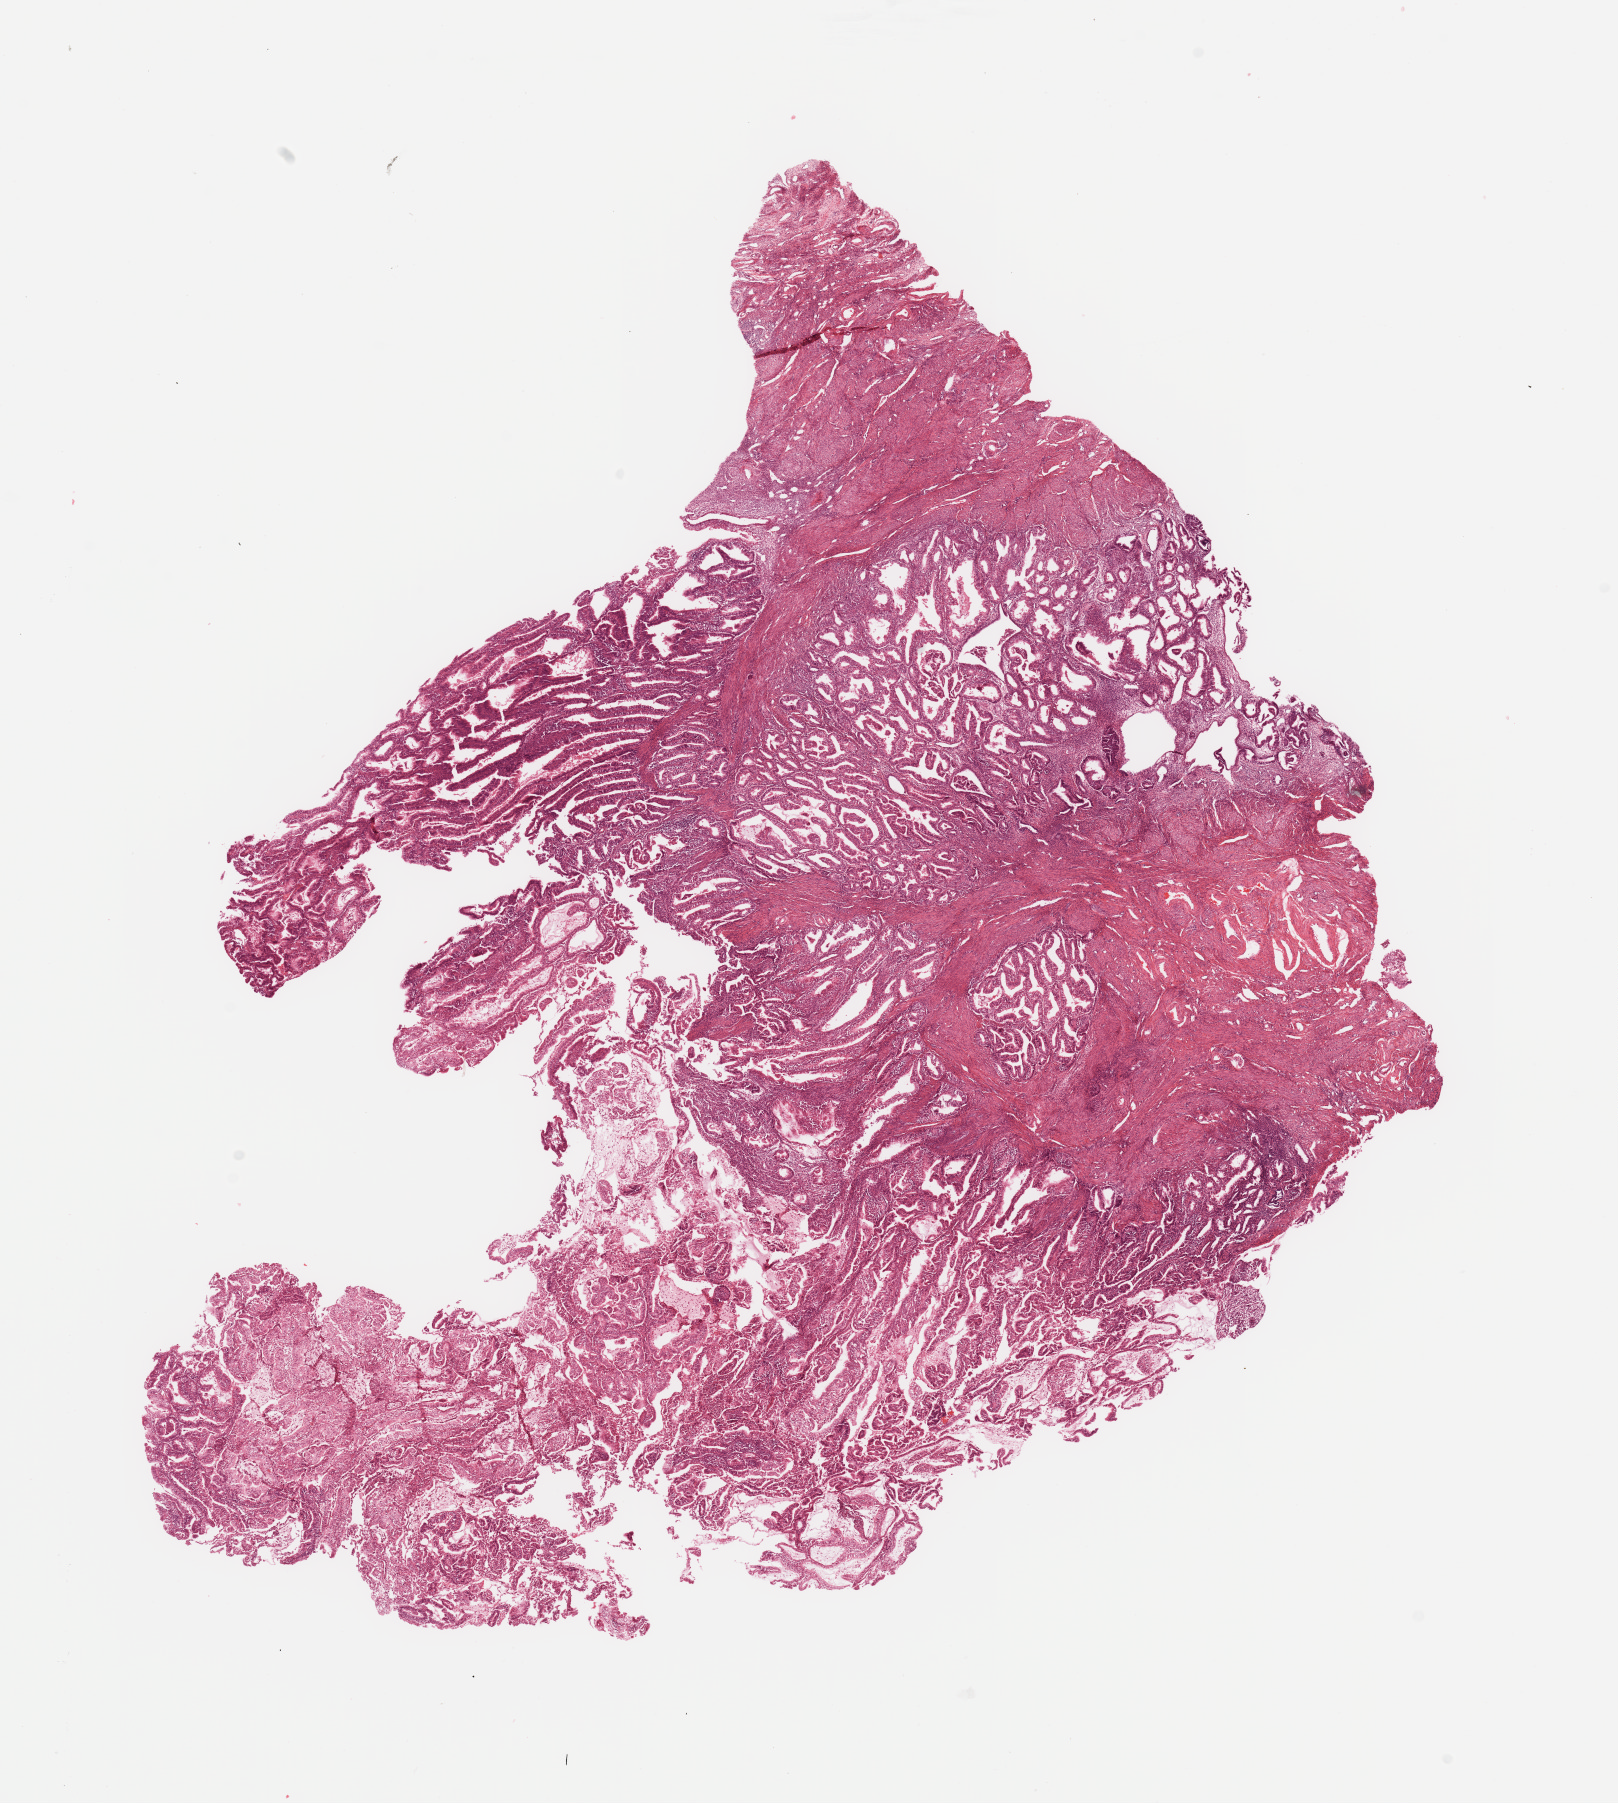
H&E whole-slide image — whole scanned area (about 12.8 x 14.3 mm) shown as a low-resolution overview; tumour tissue sample, uterus. Patient: female, age 57 years. Histologic grade: G1 (well differentiated).
AJCC pathologic stage: I. Diagnosis: Endometrioid adenocarcinoma, NOS.